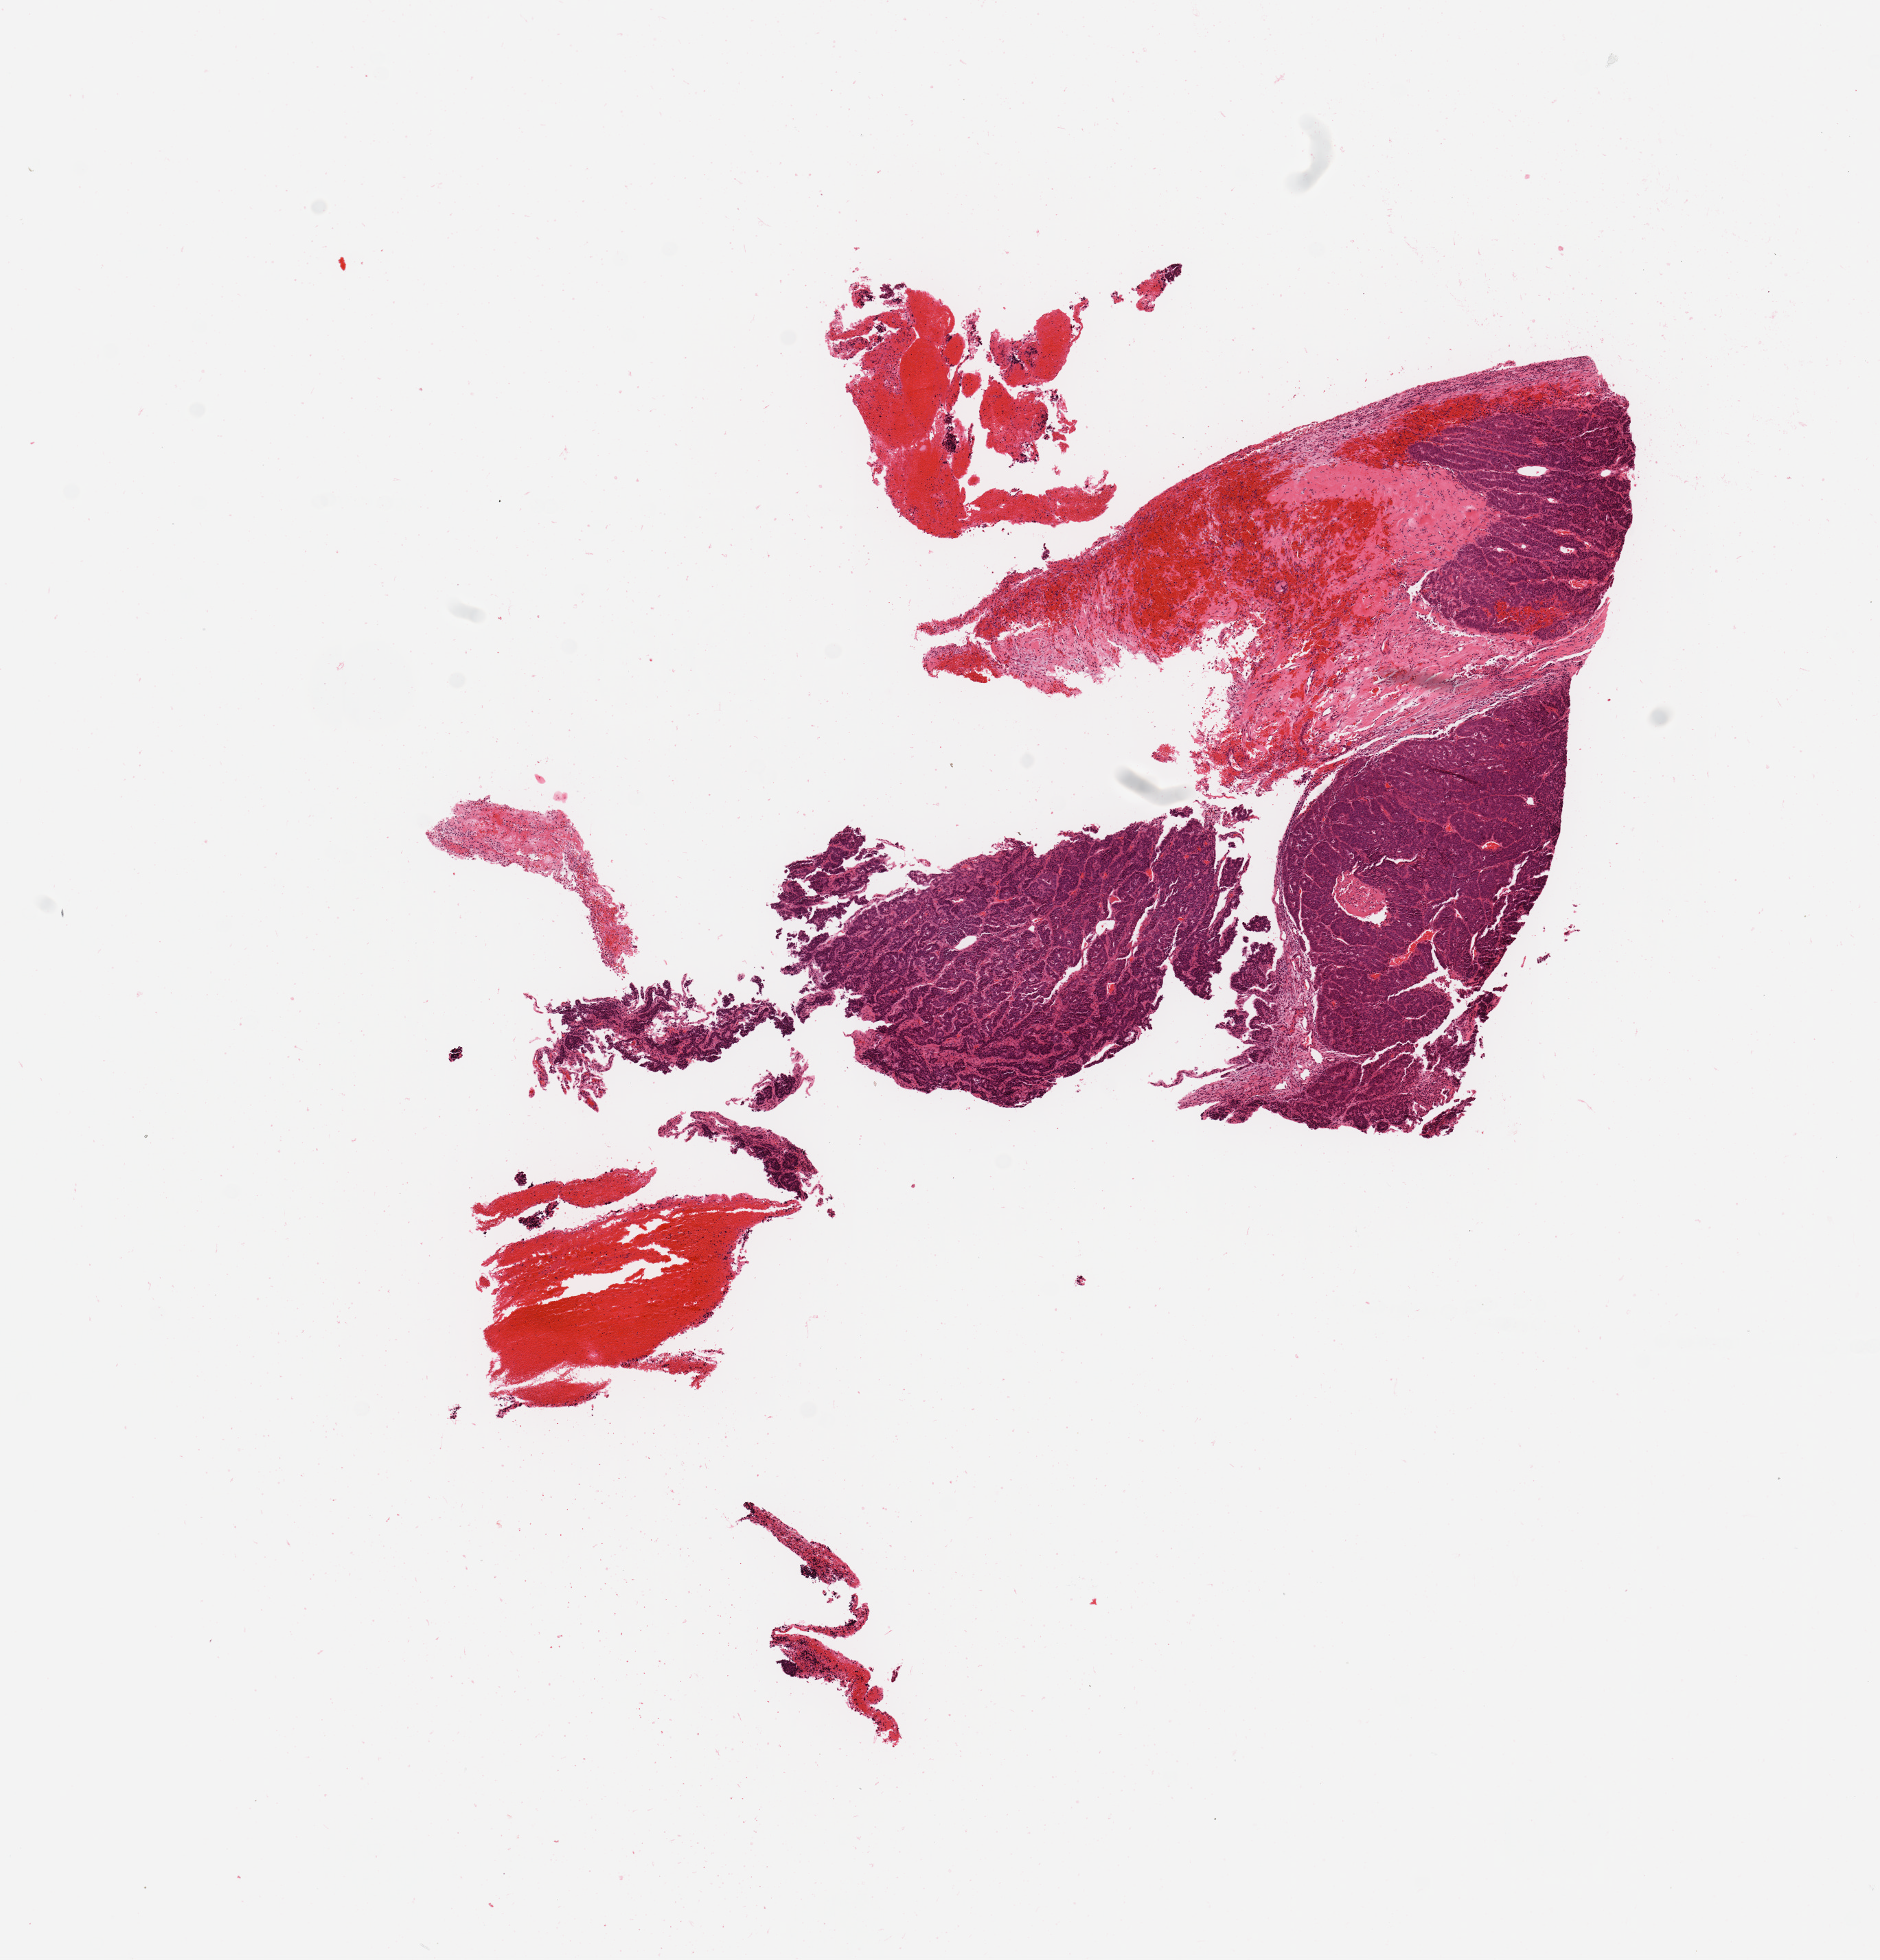
Whole-slide histology image, Hematoxylin and eosin (H&E) stained, low-resolution overview of the scanned area, about 10.8 x 11.3 mm (from a 20x scan). Tumour tissue sample, uterus. 73-year-old female patient. Histologic grade: G3 (poorly differentiated).
AJCC pathologic stage: IA. Diagnosis: Endometrioid adenocarcinoma, NOS.